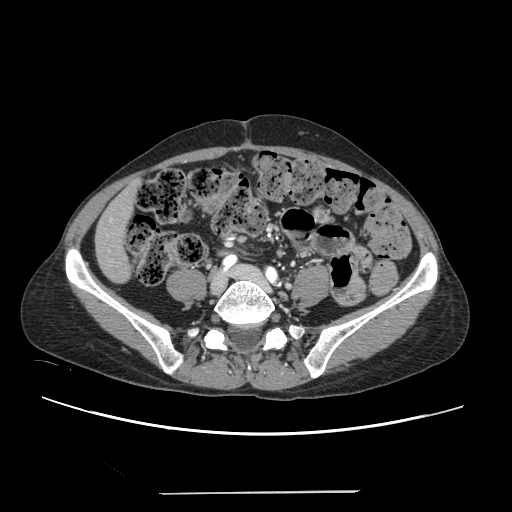
Contrast-enhanced abdominal CT, one axial slice. Position 23 of 240 along the scan axis. 120 kVp. Intravenous contrast given. Soft-tissue window (W 400 / L 40 HU). 512 × 512 image matrix, field of view 371 × 371 mm. Female patient, age 60 years. Case-level facts recorded for this patient, not image findings: diagnosis: colorectal cancer liver metastases, imaged before liver resection; multiple liver metastases: no; largest metastasis: 1.5 cm; chemotherapy before resection: yes.
Annotated regions visible in this slice (expert manual segmentation):
- liver: box from (x=97, y=186) to (x=136, y=282) px
- planned liver remnant (the part of the liver to remain after resection): (x=97, y=185)–(x=136, y=282)
- portal vein (with intrahepatic branches): (x=109, y=218)–(x=112, y=221)